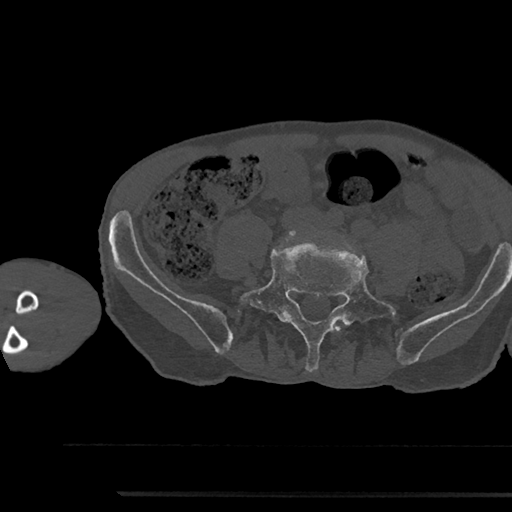
CT including the spine, one axial slice; slice 356 of 797 in the series (ordered by position); reconstruction kernel Br40s/3; bone window (W 1800 / L 400 HU); 0.5 mm slice thickness; 512 × 512 image matrix, field of view 367 × 367 mm. Male patient, age 79 years. Case-level facts recorded for this patient, not image findings: primary cancer: prostate.
Annotated regions visible in this slice (semi-automatically segmented with operator editing):
- L4 vertebra: bounding box <334,325,342,332> (left, top, right, bottom; pixels)
- L5 vertebra: <240,247,398,371>